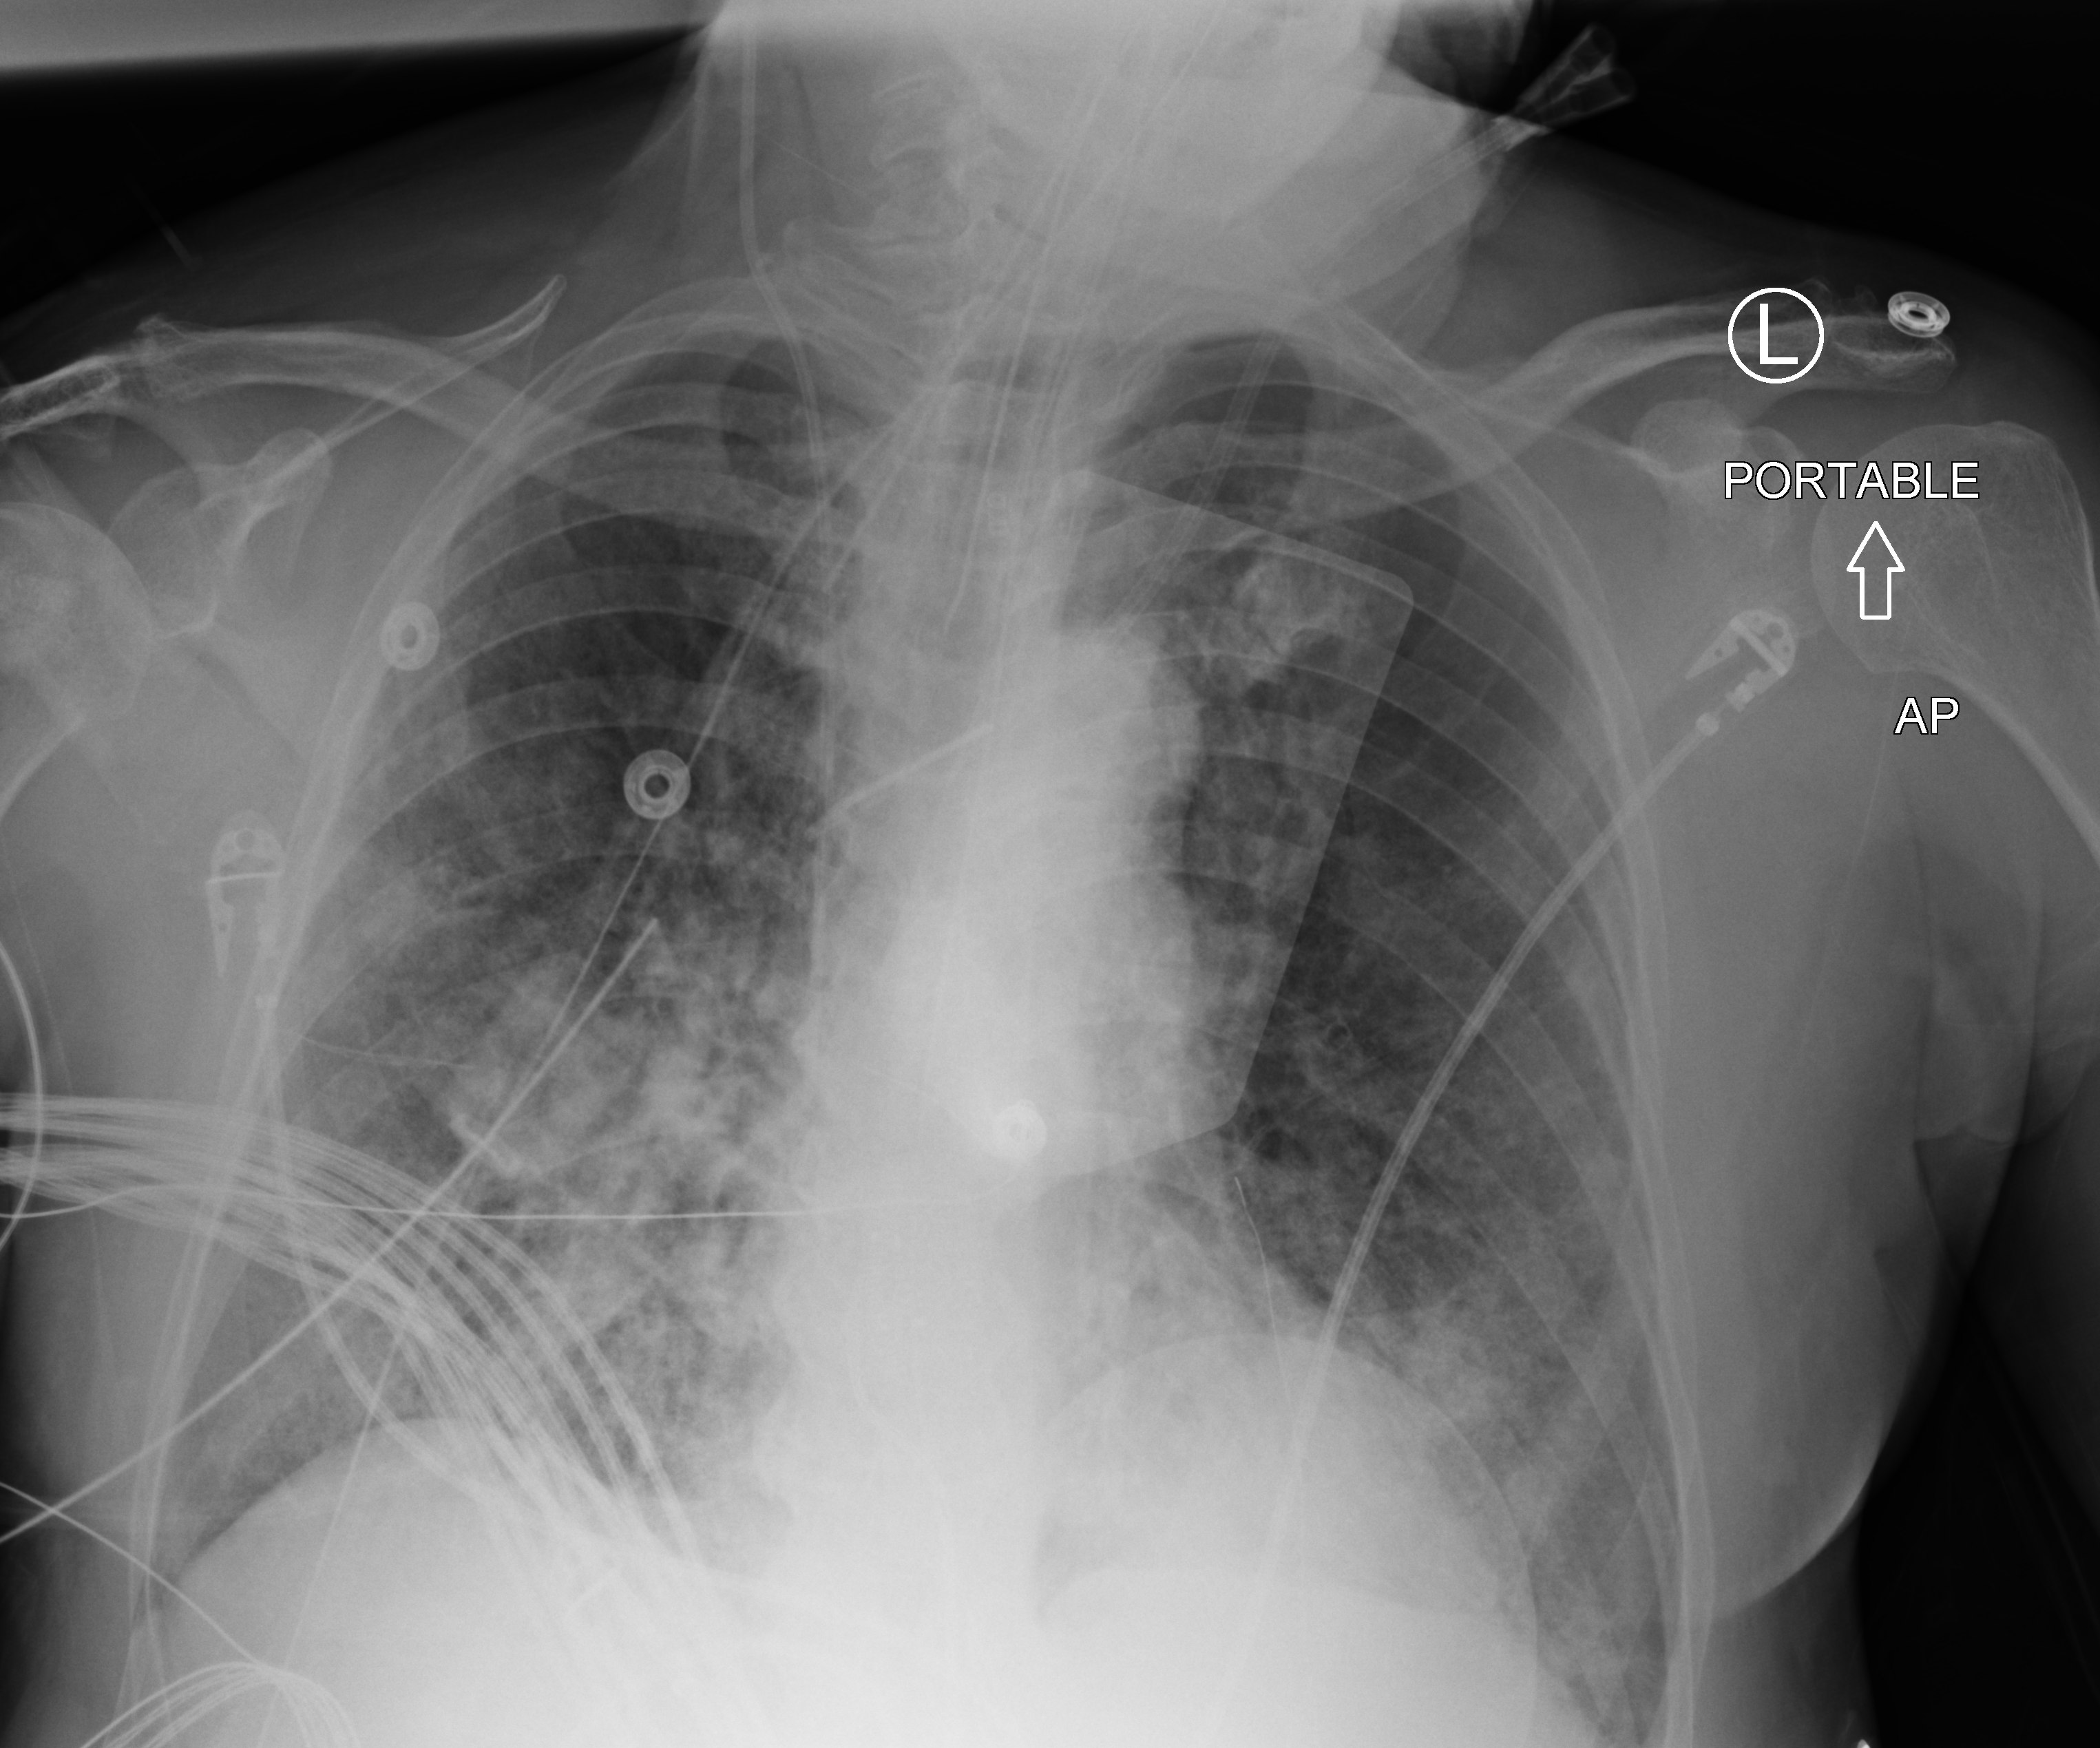
Bedside chest radiograph (computed radiography); anteroposterior (AP) projection. Male patient hospitalised with COVID-19, age 60–74 years.
From the hospital-stay record, not from the radiograph (when in the stay this image was taken is not recorded):
- admitted to intensive care during this hospital stay: yes
- diabetes (admission record): no
- mechanically ventilated during this hospital stay: yes